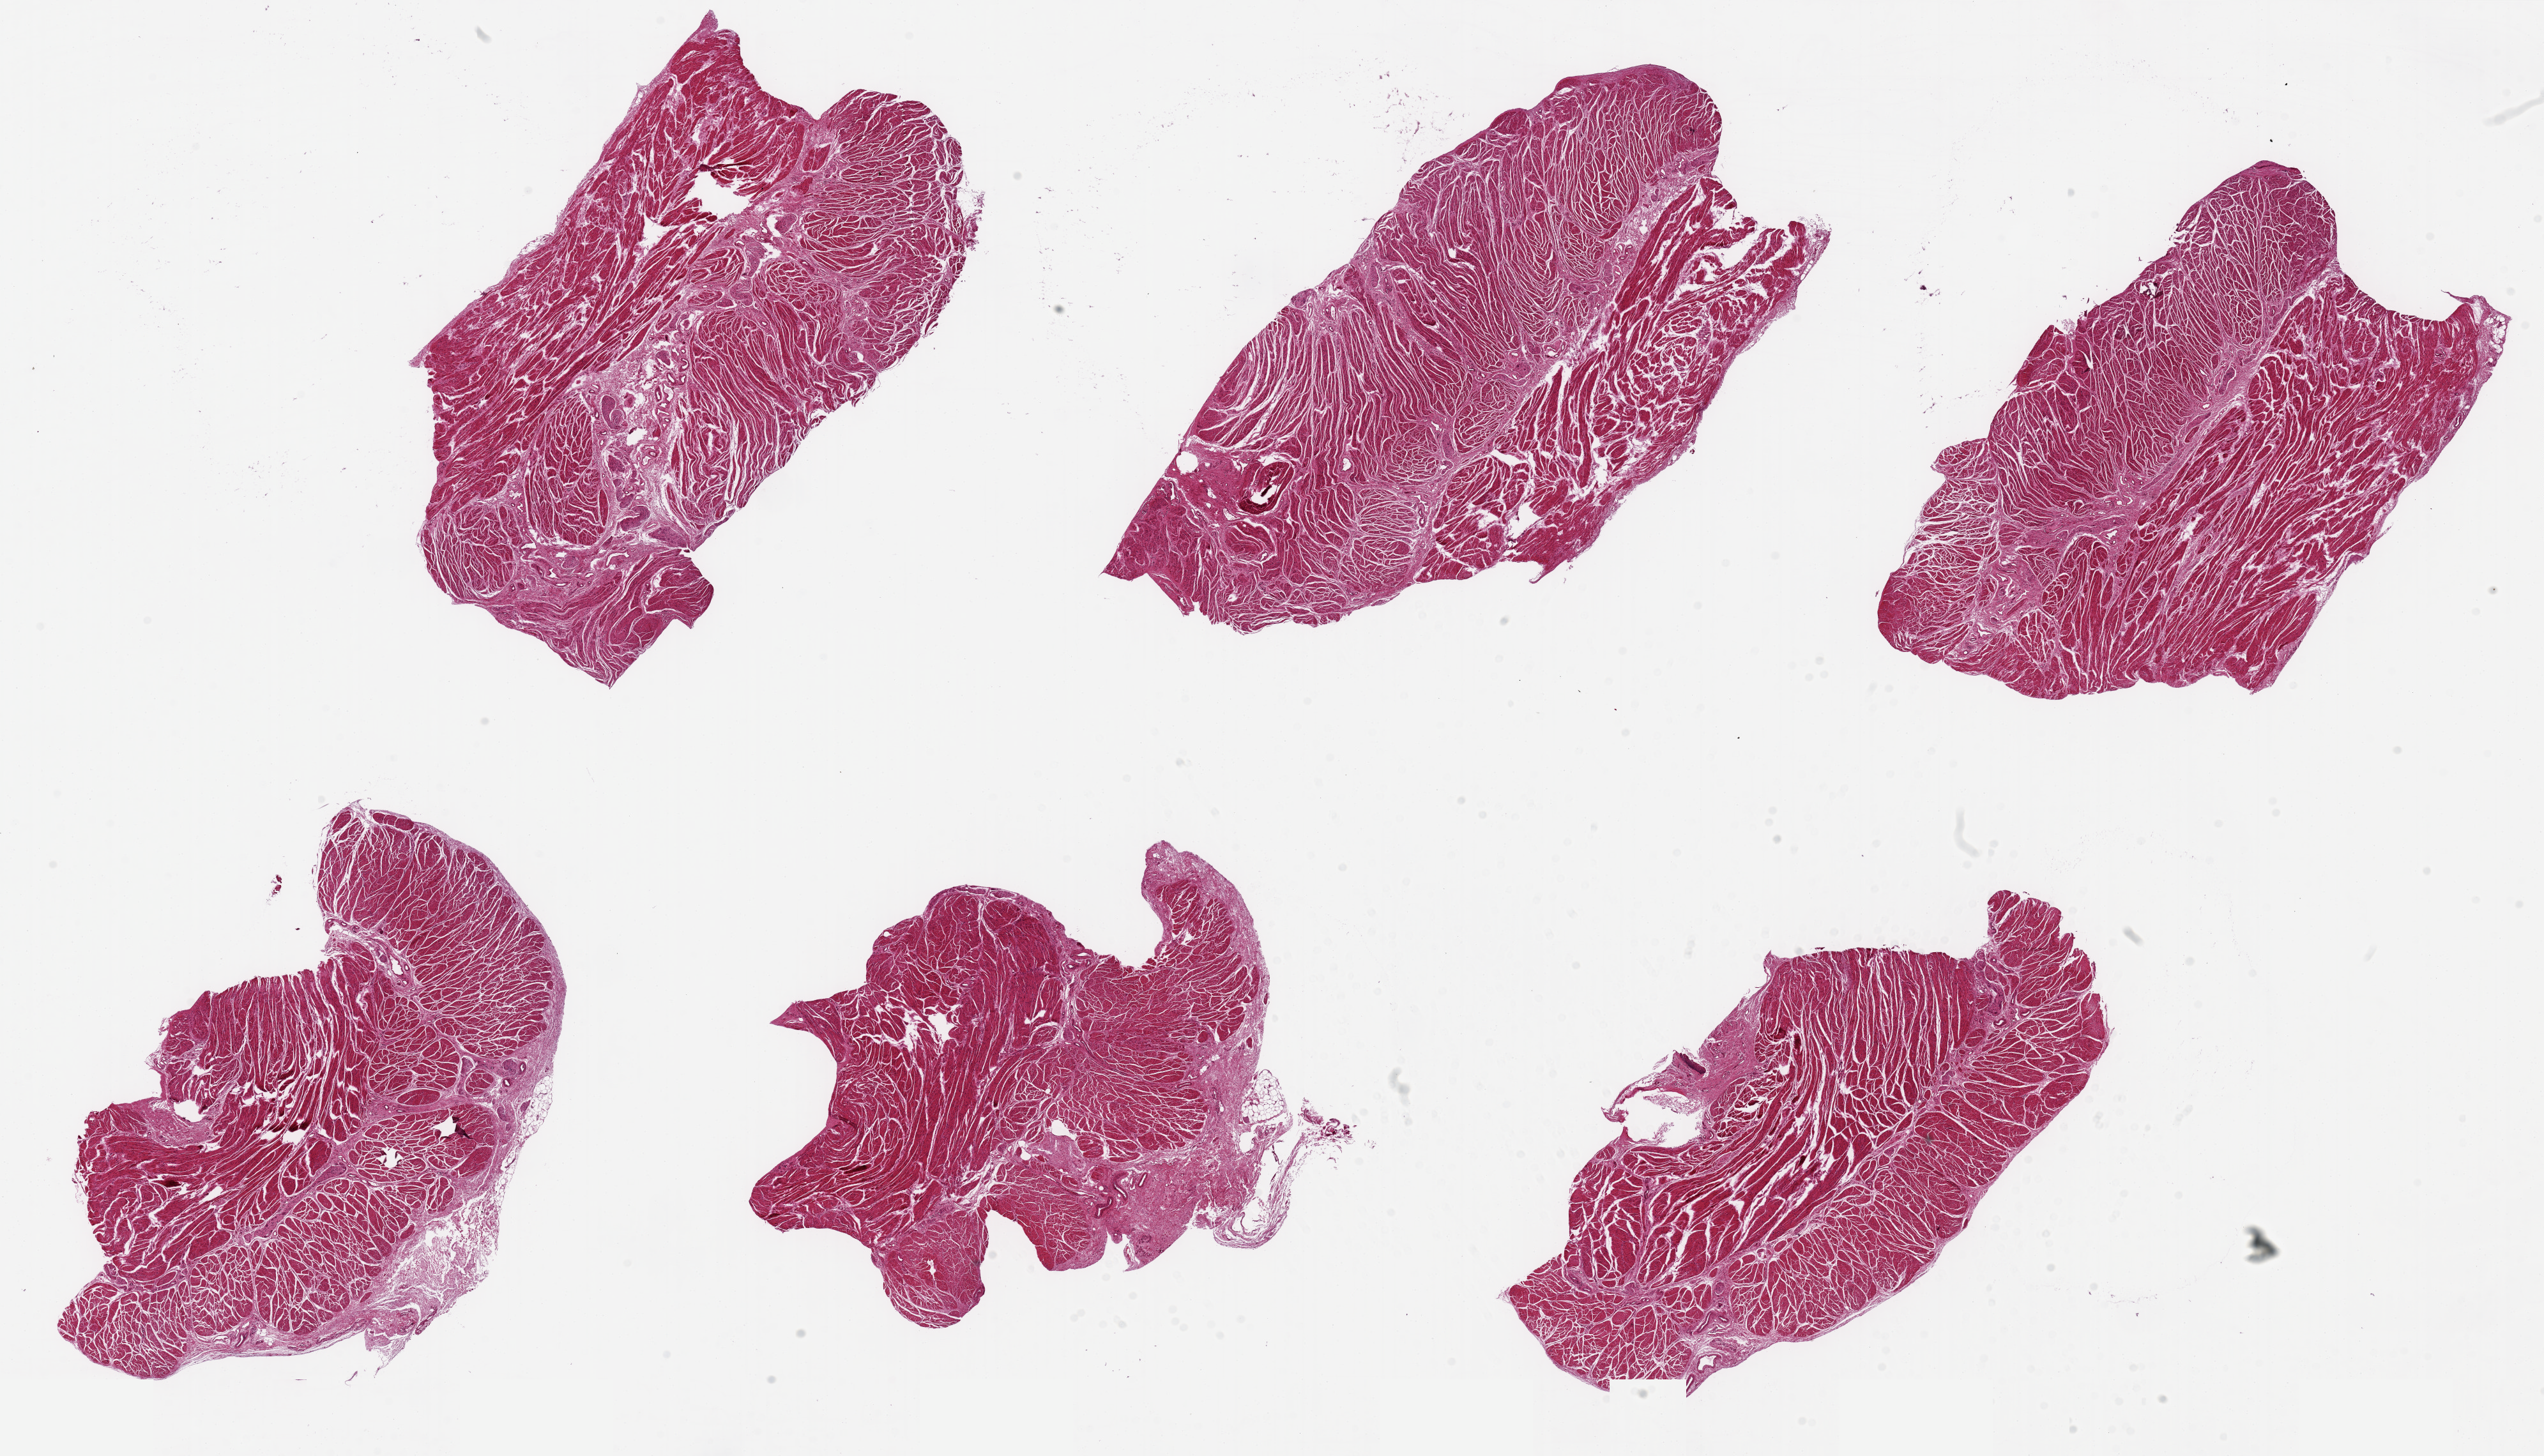
Whole-slide image, hematoxylin and eosin (H&E) stain, a low-resolution overview of the entire scanned area, about 31.5 x 18.0 mm (acquisition: 20x scan), PAXgene-fixed paraffin-embedded (PFPE) section, section of gastroesophageal junction (target tissue), donor tissue sample.
Pathologist's review note for this sample: 6 pieces, up to 9x5mm; good pure muscularis propria in all.